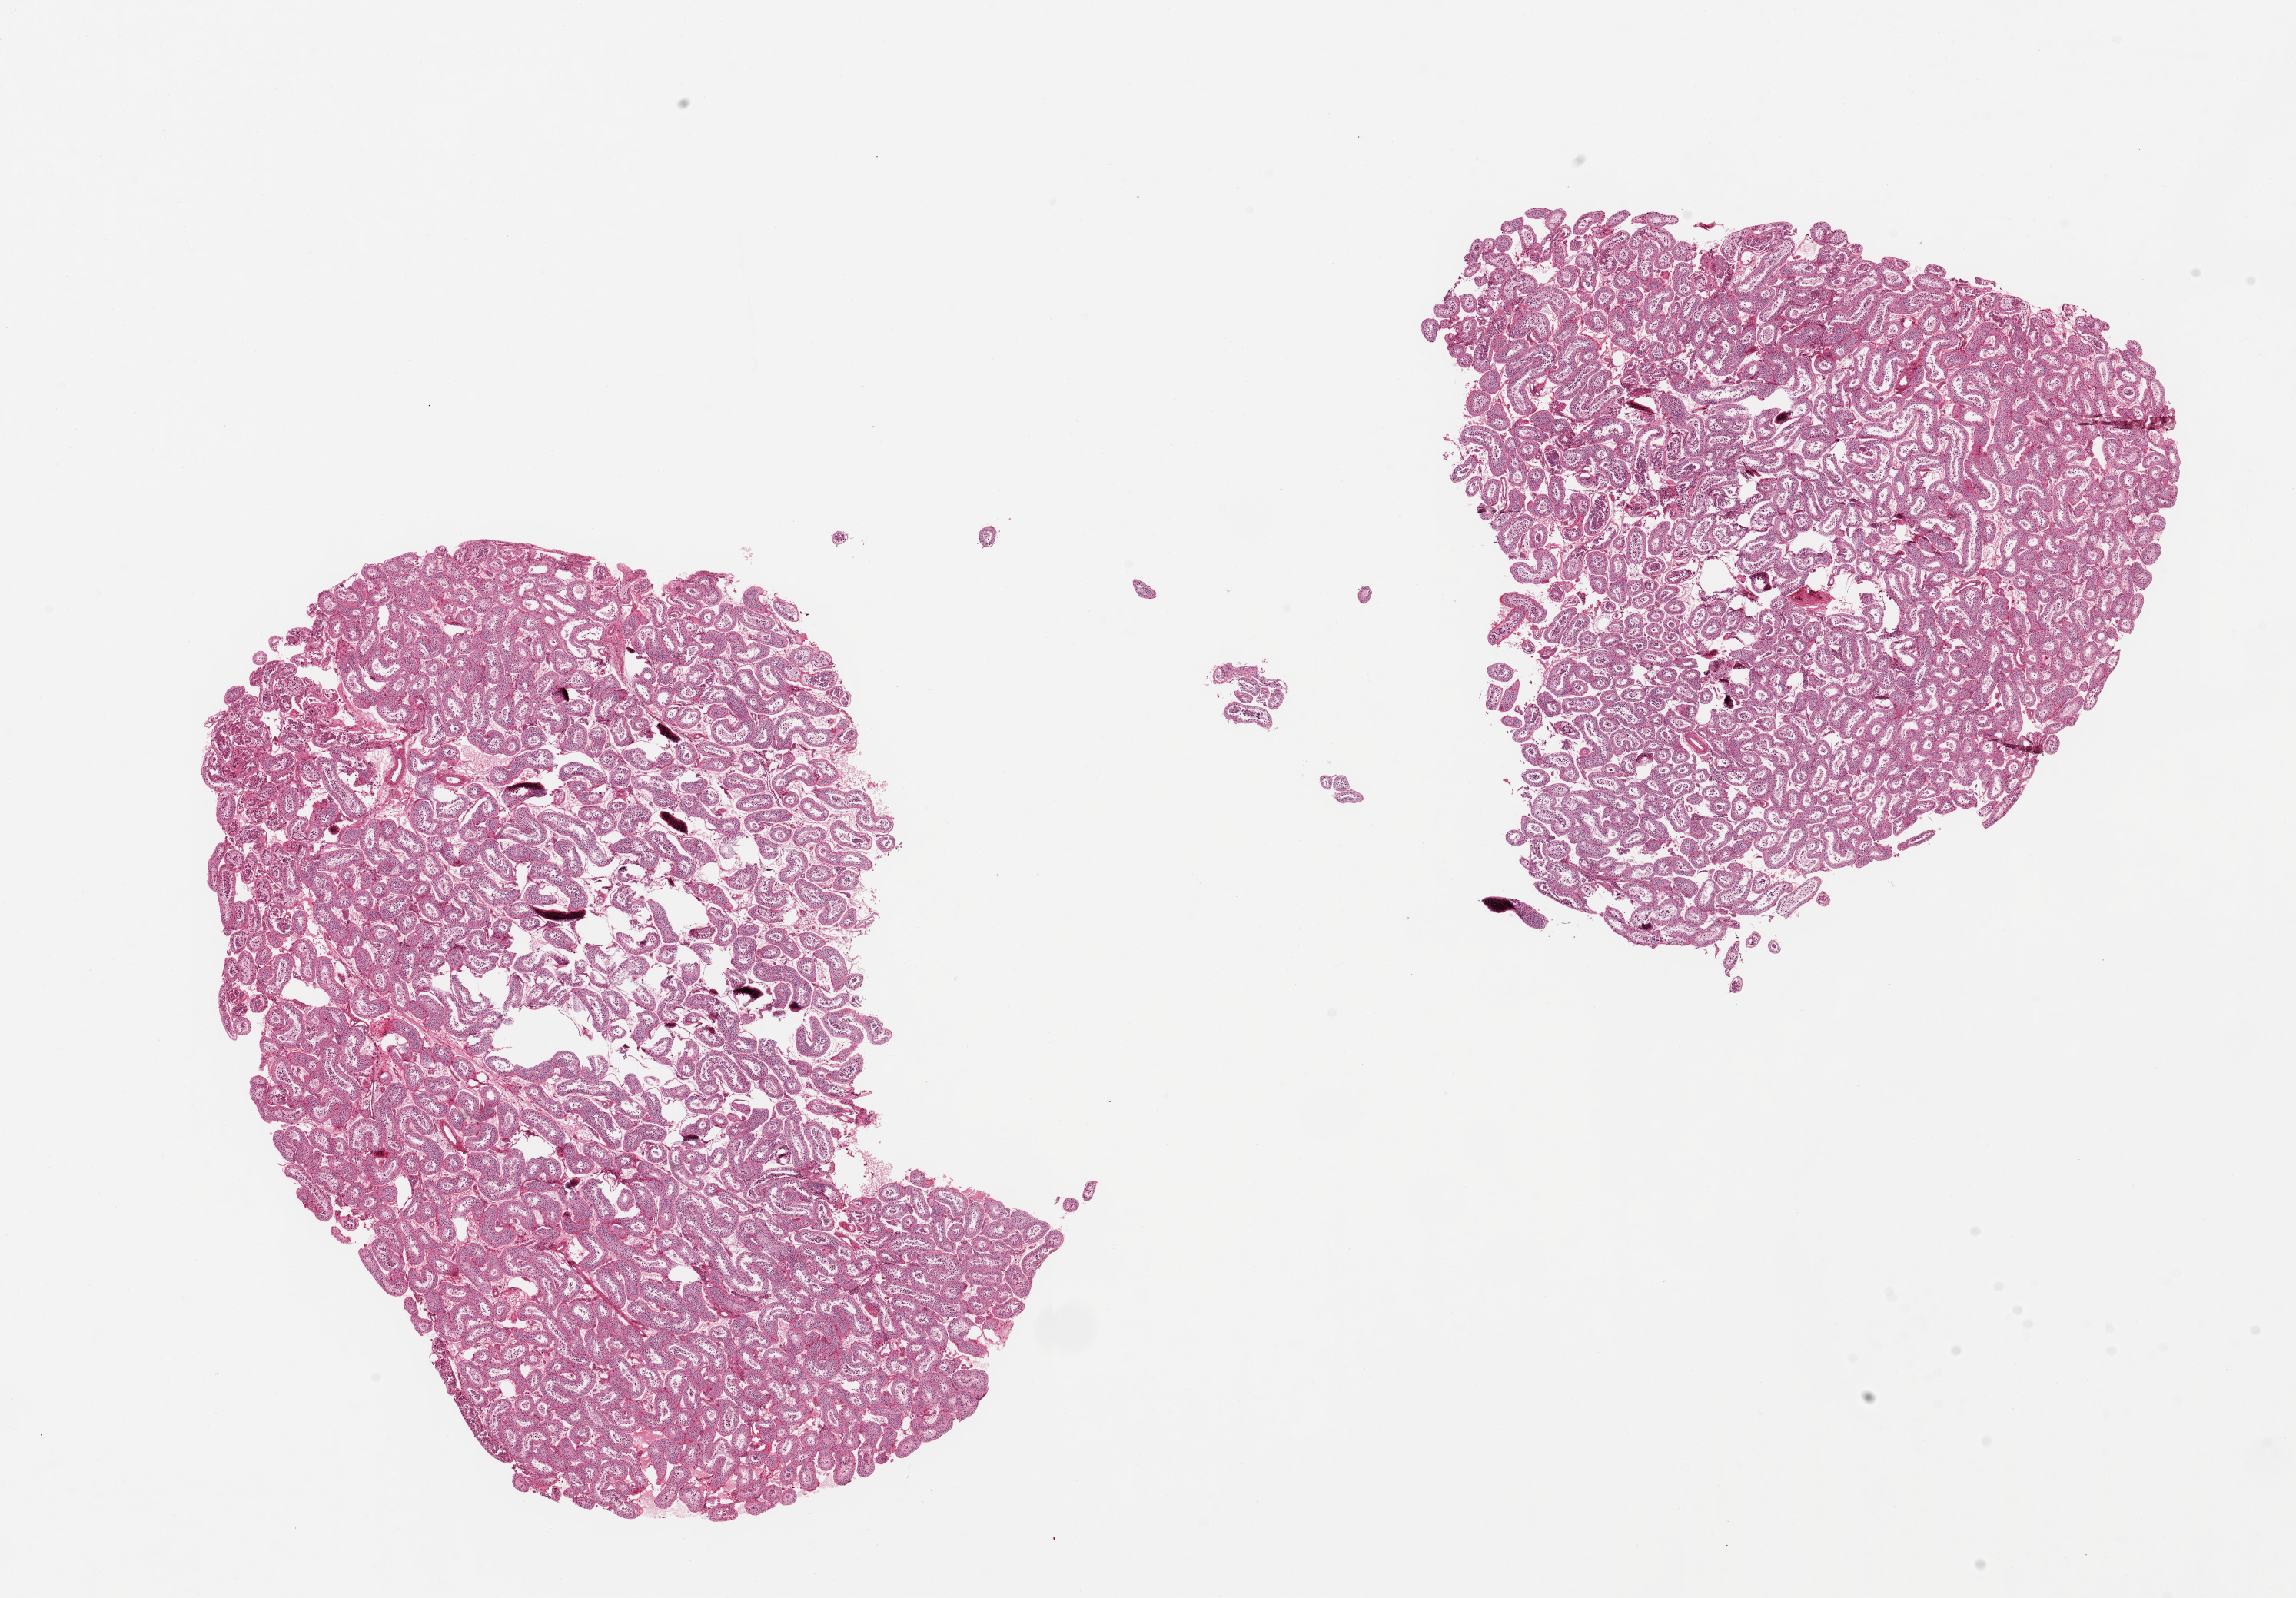
Whole-slide image, hematoxylin and eosin (H&E) stain, low-resolution overview of the scanned area, about 23.6 x 16.4 mm (slide scanned at 20x); PAXgene-fixed paraffin-embedded (PFPE) section; section of testis (target tissue); donor tissue sample. Male donor.
- review note (as recorded): 2 pieces ~10x8mm. Spermatogenesis markedly reduced